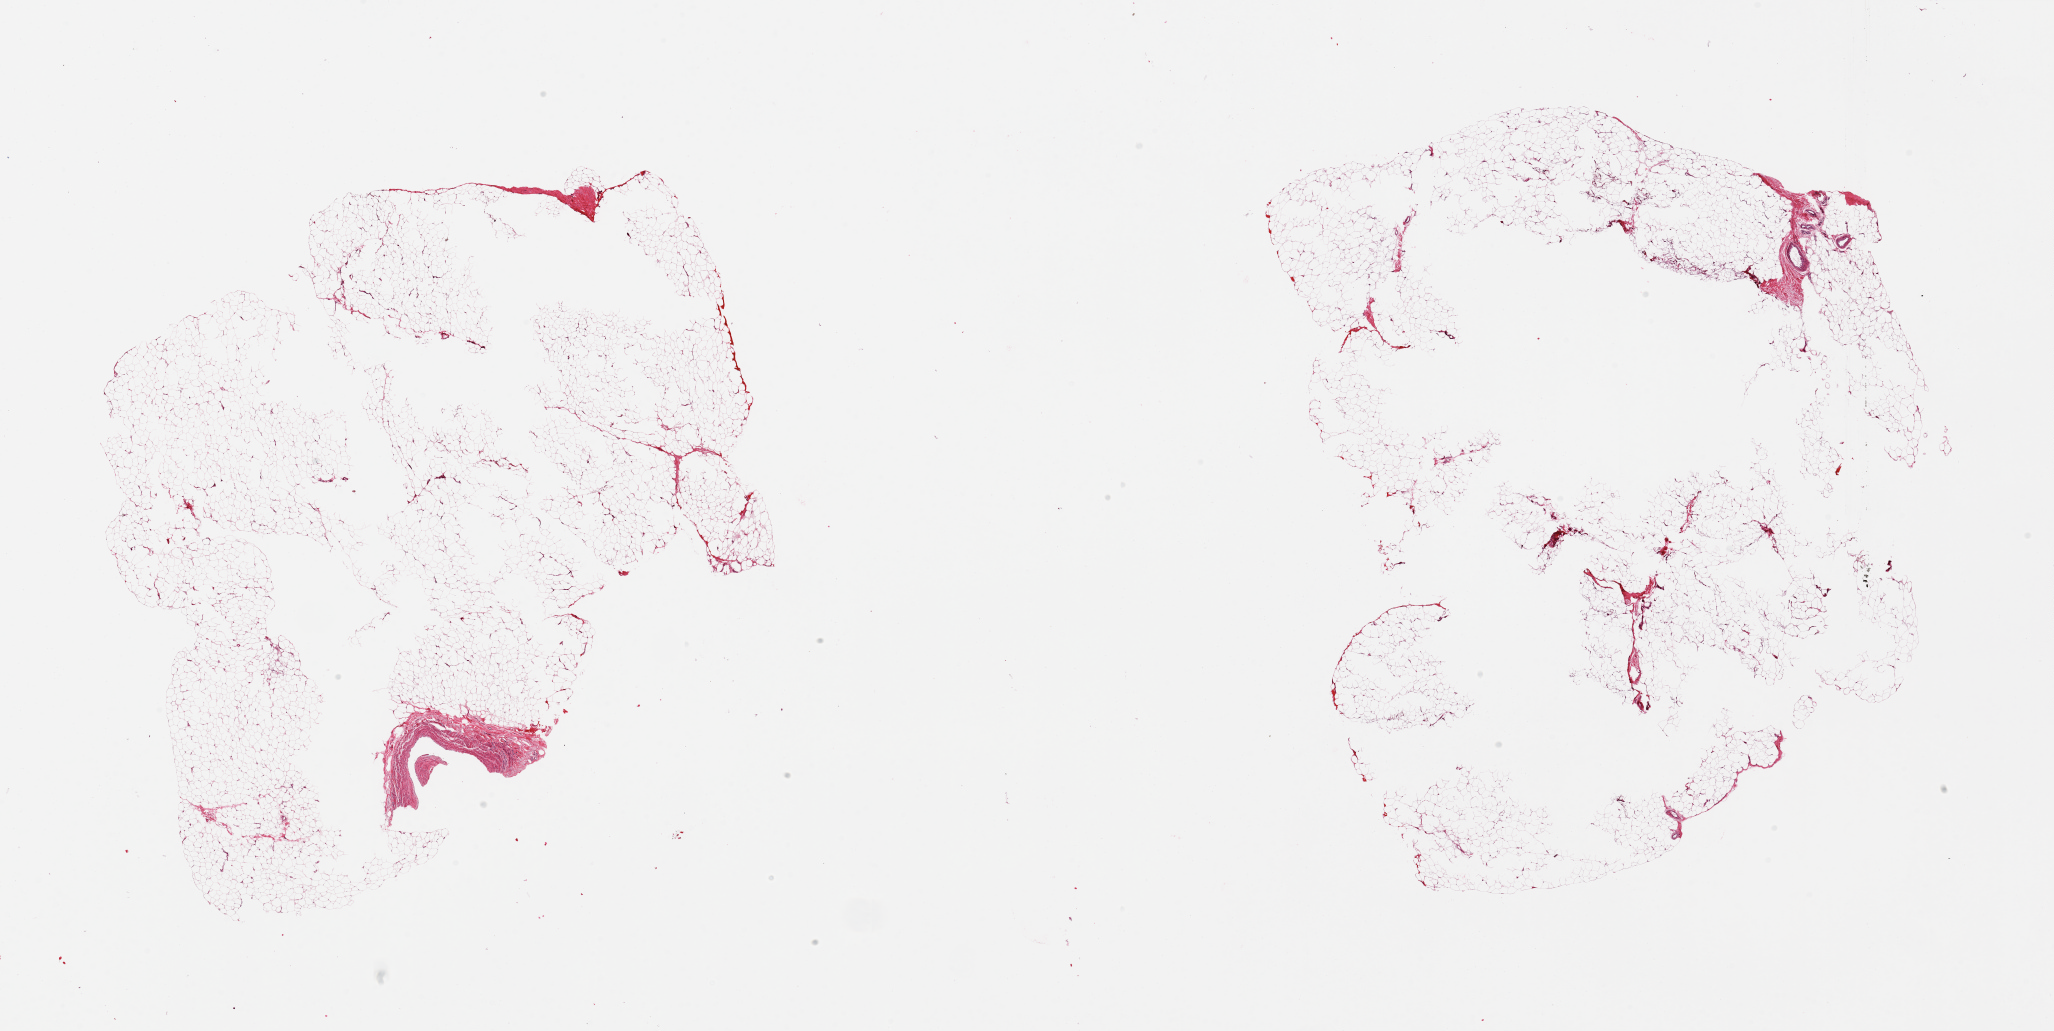
Whole-slide image, hematoxylin and eosin (H&E) stain, a low-resolution overview of the entire scanned area, about 32.5 x 16.3 mm (slide scanned at 20x). PAXgene-fixed, paraffin-embedded tissue. Section of adipose tissue (target tissue). Tissue donor sample. Female donor.
Reviewer comment on this tissue sample: 2 pieces; large central defects (?poor fixation), portion of large vessel in 1 piece.